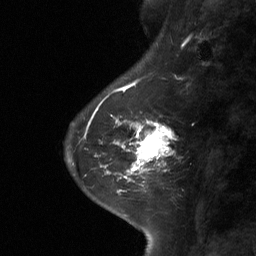
Breast MRI (dynamic contrast-enhanced), one sagittal slice. Position 20 of 64 along the scan axis. Dynamic contrast-enhanced study with each time point stored as its own series, time point 2 of 3 at this slice position (early post-contrast, ordered by acquisition time). 1.5 T. TE 4.8 ms, TR 27 ms. 256 × 256 image matrix, field of view 180 × 180 mm. Female patient, age 42 years. From the clinical record (not read from this slice): setting: breast cancer imaged before/during neoadjuvant chemotherapy; receptor status: triple-negative.
Annotated regions visible in this slice (semi-automatic segmentation, software-assisted and operator-edited):
- analysis volume of interest (the breast-tissue region the enhancement analysis was run in; not a lesion): box from (x=111, y=104) to (x=177, y=178) px
- tumour enhancement mask (voxels above the 90 % enhancement threshold inside the analysis volume of interest): (x=111, y=115)–(x=174, y=178)